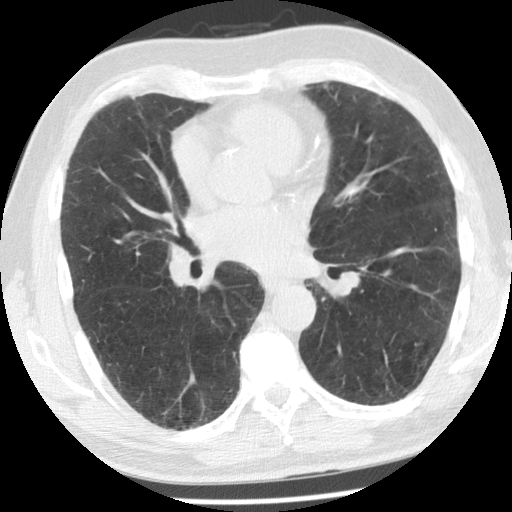
Axial slice from a low-dose chest CT screening exam; baseline annual screen; lung window (W 1500 / L -600 HU); 2.5 mm slice thickness; standard (soft-tissue) reconstruction kernel (STANDARD). Male, age 66 years at enrolment. Former smoker at enrolment.
Expert reader's lesion annotation, bounding box (x1, y1, x2, y2) in pixels: (310, 73, 344, 103). The exam's reader record, not a measurement of the box and not confirmed to be the same lesion: non-calcified nodule or mass ≥4 mm, lingula, 5 × 4 mm, smooth margins, soft tissue attenuation. Official screen result: positive, change unspecified: nodule(s) >= 4 mm or enlarging nodule(s), mass(es), or other non-specific abnormalities suspicious for lung cancer. Lung cancer was diagnosed 449 days after this screen: adenocarcinoma, NOS, left upper lobe, moderately differentiated (G2), stage IIB (AJCC 6th edition), 9 mm at pathology.